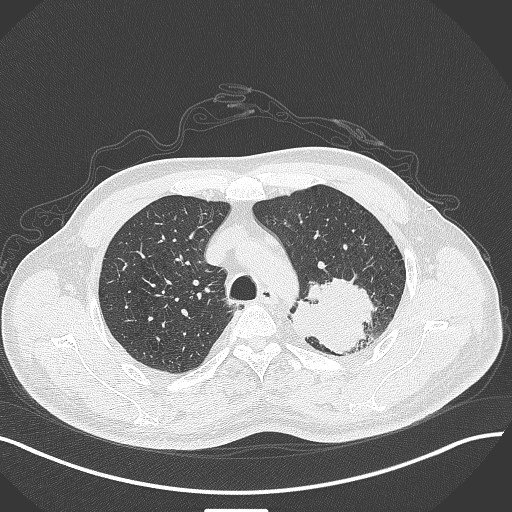
Chest CT, one axial slice. Slice 326 of 429 in the series (ordered by position). Lung window (W 1500 / L -600 HU). 1 mm slice thickness. 512 × 512 image matrix. Male patient, age 55 years. From the clinical record (not read from this slice): clinical TNM (as recorded): T3 N0 M1c; histopathological grade: G3.
Structures marked on this image (bounding box drawn by a radiologist):
- lung tumour (recorded histology: adenocarcinoma): box from (x=289, y=272) to (x=375, y=356) px